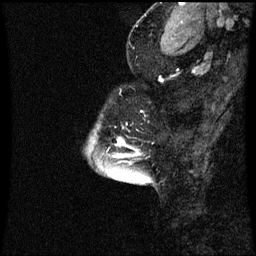
Breast MRI (dynamic contrast-enhanced), one sagittal slice; dynamic contrast-enhanced series, image 2 of 3 at this slice position (ordered by acquisition); 1.5 T; TE 4.2 ms, TR 8.9 ms; 2 mm slice thickness; 256 × 256 image matrix, field of view 200 × 200 mm. Patient: female, 43 years. From the clinical record (not read from this slice): setting: breast cancer imaged before/during neoadjuvant chemotherapy; receptor status: HR-positive, HER2-negative.
Outlined on this slice (semi-automatically segmented with operator editing):
- analysis volume of interest (the breast-tissue region the enhancement analysis was run in; not a lesion): box from (x=96, y=124) to (x=143, y=159) px
- tumour enhancement mask (voxels above the 70 % enhancement threshold inside the analysis volume of interest): (x=118, y=140)–(x=125, y=145)